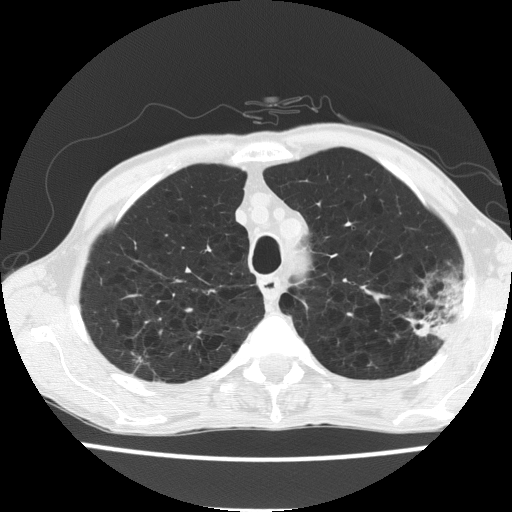
Low-dose screening chest CT, axial slice, baseline screening round, lung window (W 1500 / L -600 HU), 120 kVp, slice 40 of 187 in the series. Male participant, aged 60 years at enrolment. Current smoker at enrolment.
Expert reader's lesion annotation, bounding box [x1, y1, x2, y2] px = [393, 271, 465, 345]. Screening reader's record for this exam: no non-calcified nodule ≥4 mm recorded. Official screen result: negative screen, minor abnormalities not suspicious for lung cancer.